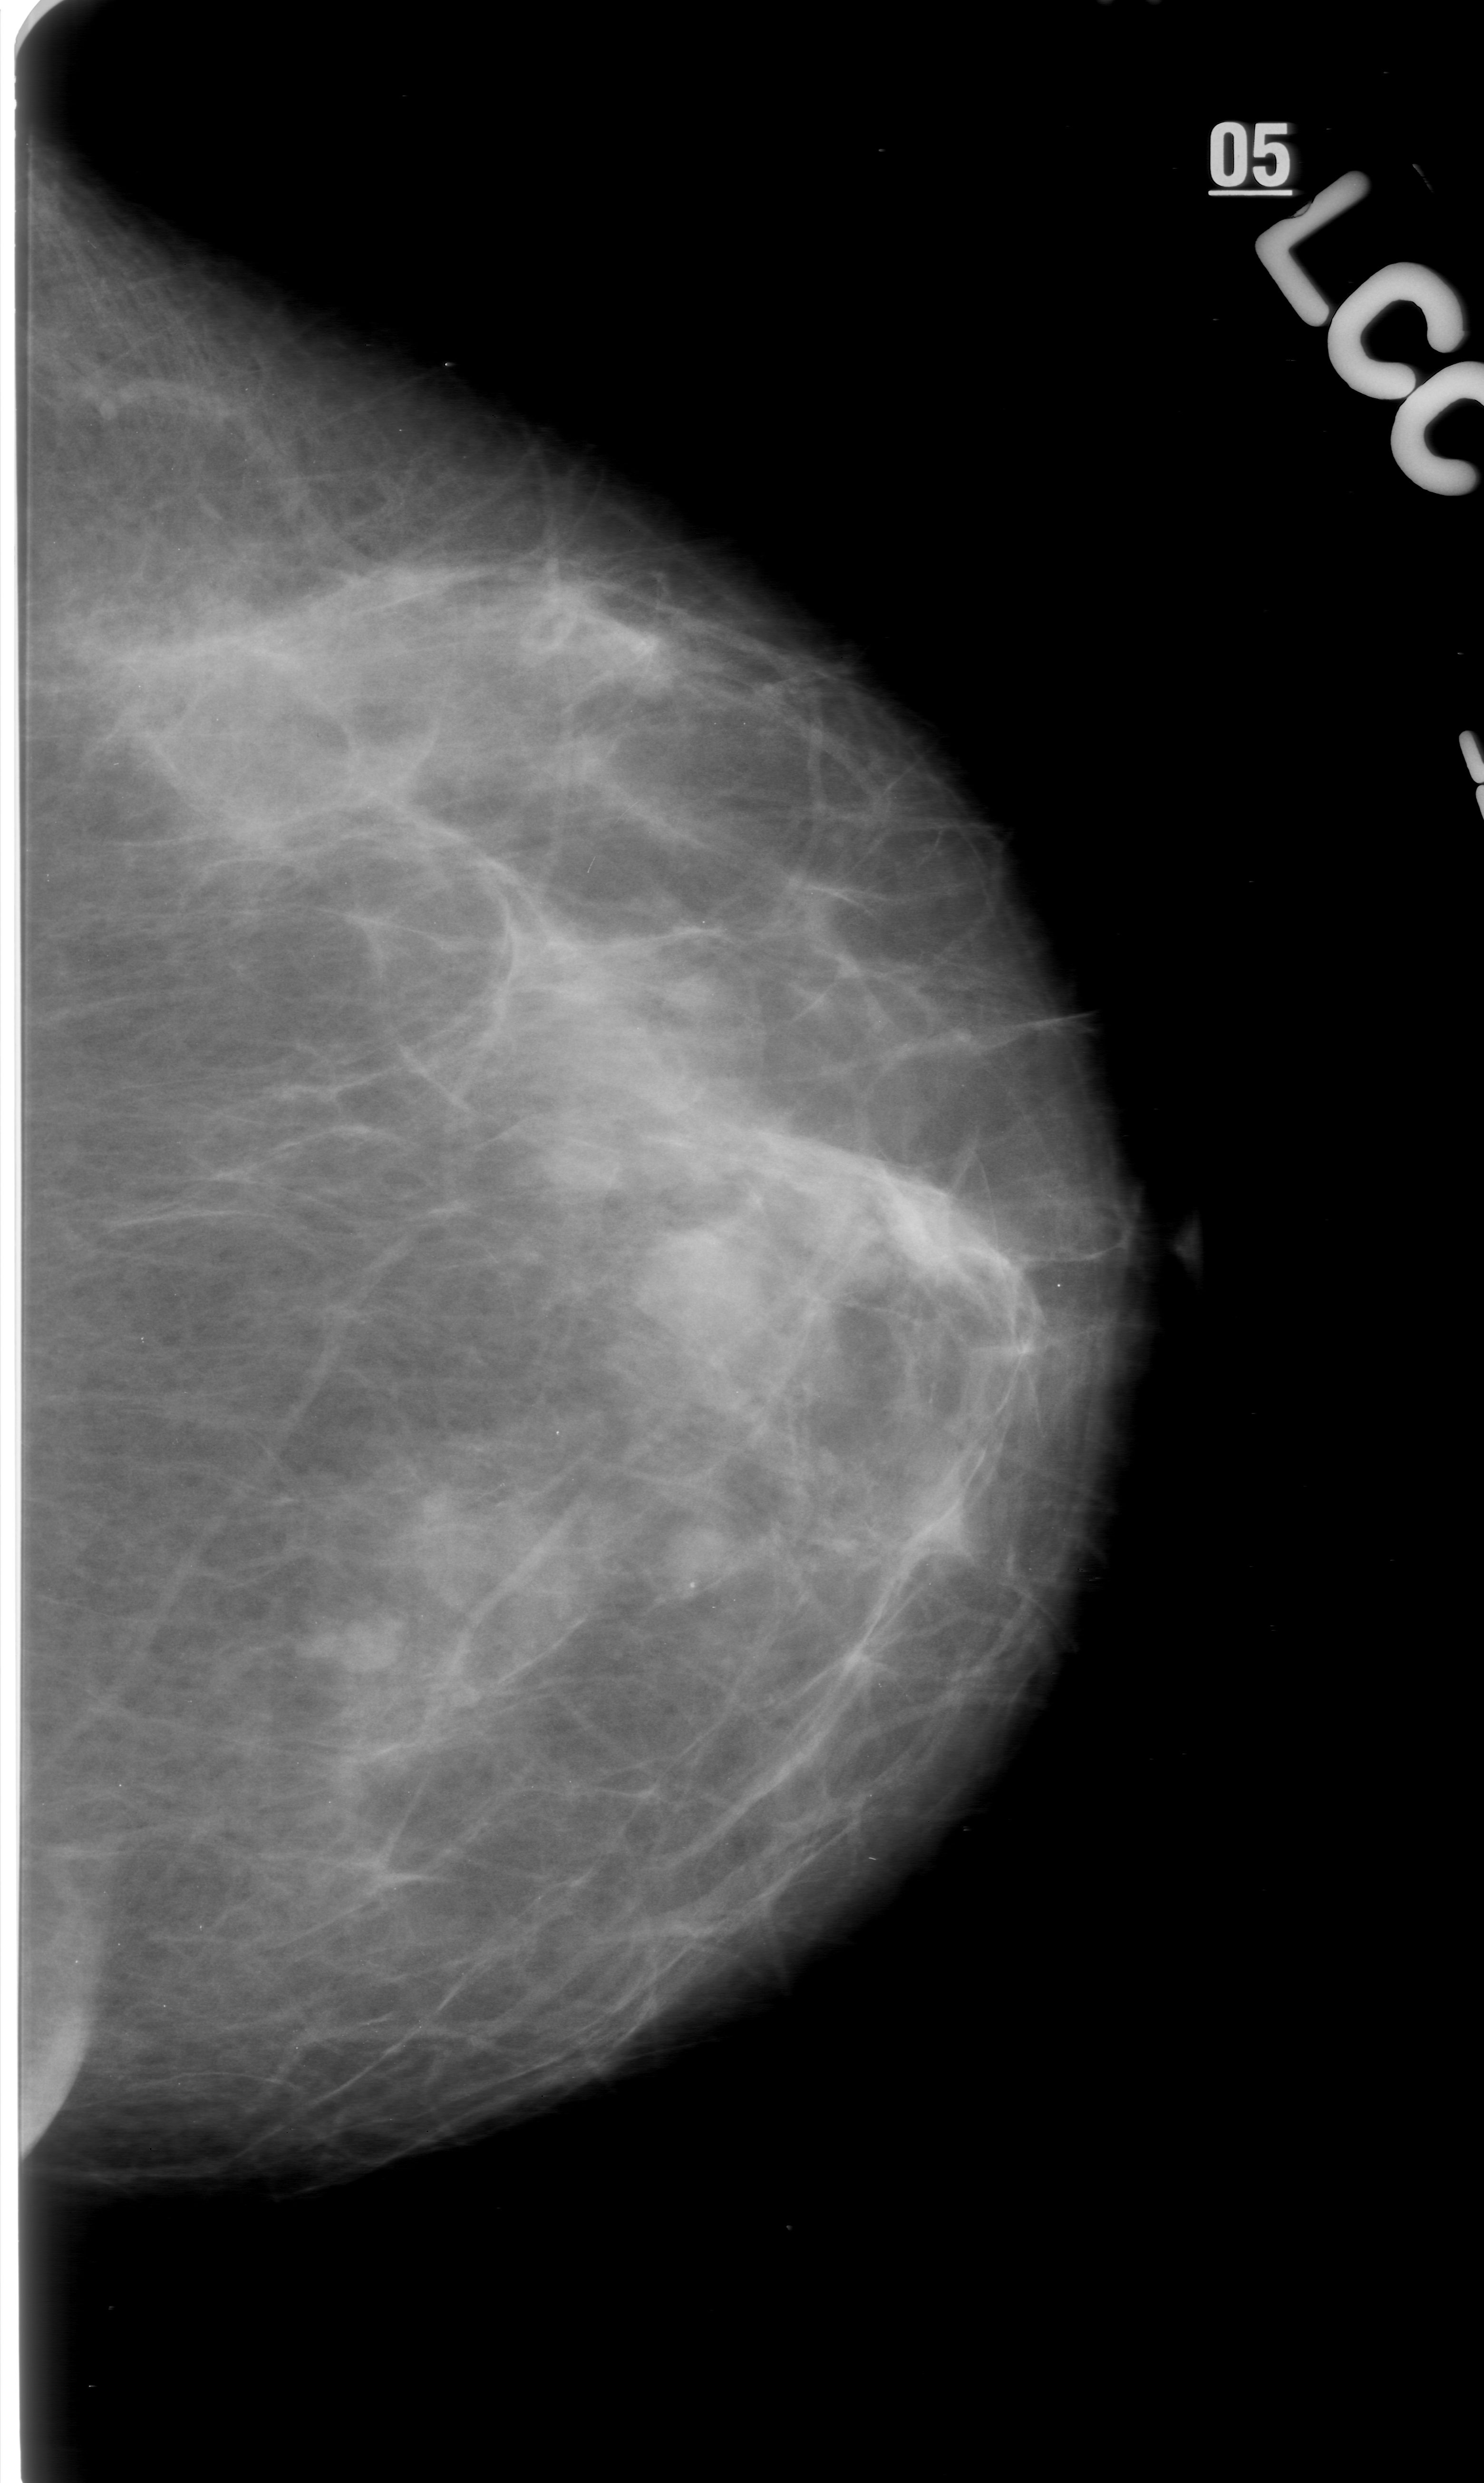
Mammogram (digitized film), left breast, CC view.
Marked findings (only marked abnormalities are described; nothing is implied about the rest of the image): mass, shape irregular, margins ill defined; BI-RADS assessment category 0 (incomplete: needs additional imaging); subtlety rating 5 on a 1 (subtle) to 5 (obvious) scale; pathology (as recorded): benign.